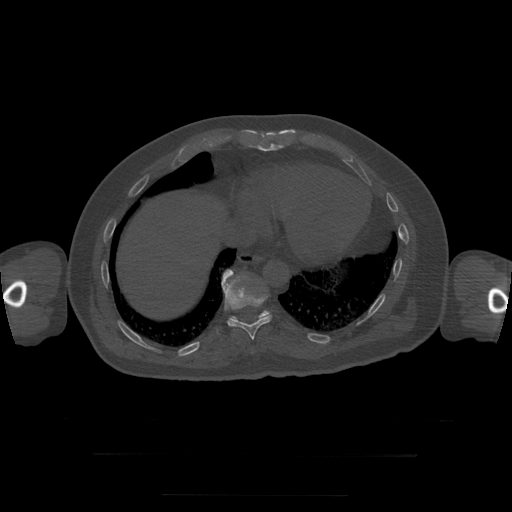
CT including the spine, one axial slice. Position 118 of 397 along the scan axis. Reconstruction kernel STANDARD. 120 kVp. Bone window (W 1800 / L 400 HU). 1.25 mm slice thickness. 512 × 512 image matrix. Patient age 73 years. Case-level facts recorded for this patient, not image findings: primary cancer: prostate.
Outlined on this slice (semi-automatically segmented with operator editing):
- T10 vertebra: bounding box <222,270,272,340> (left, top, right, bottom; pixels)
- T11 vertebra: <232,274,270,322>